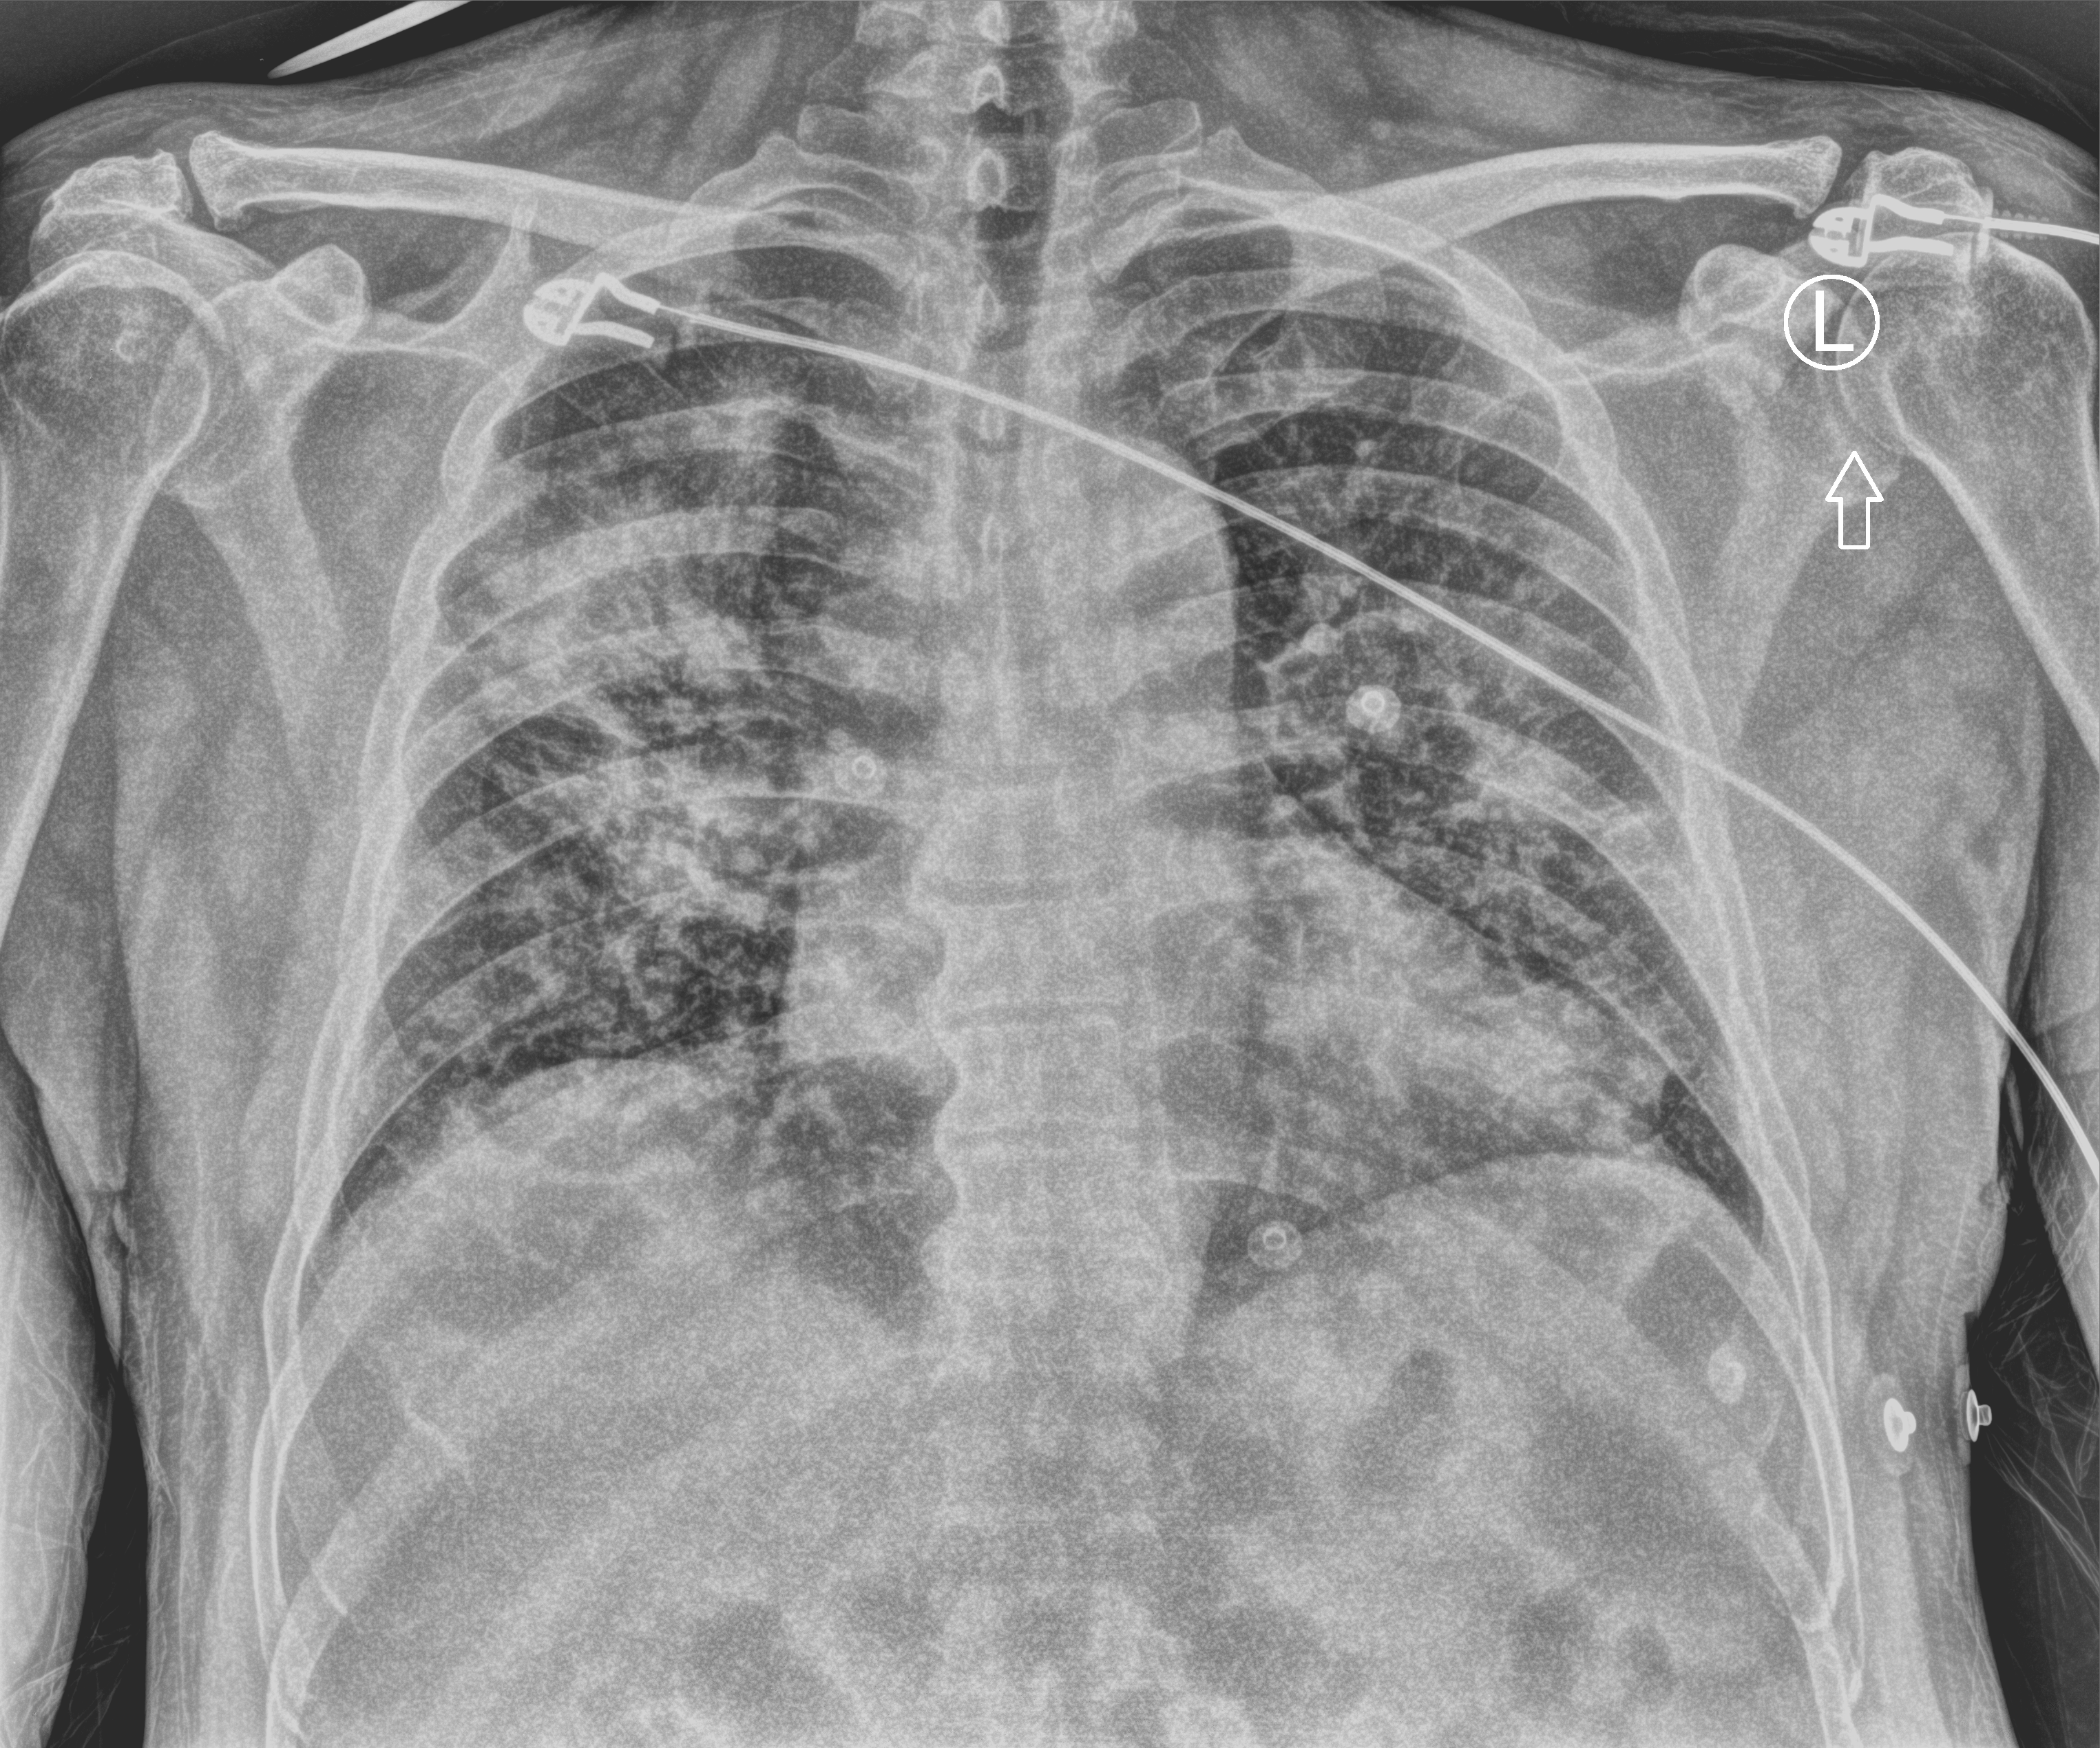
Chest X-ray (portable); anteroposterior (AP) projection. Male patient hospitalised with COVID-19, age 18–59 years.
Hospital-stay facts (about this admission, not read from this image; timing relative to this image not recorded):
- admitted to intensive care during this hospital stay: no